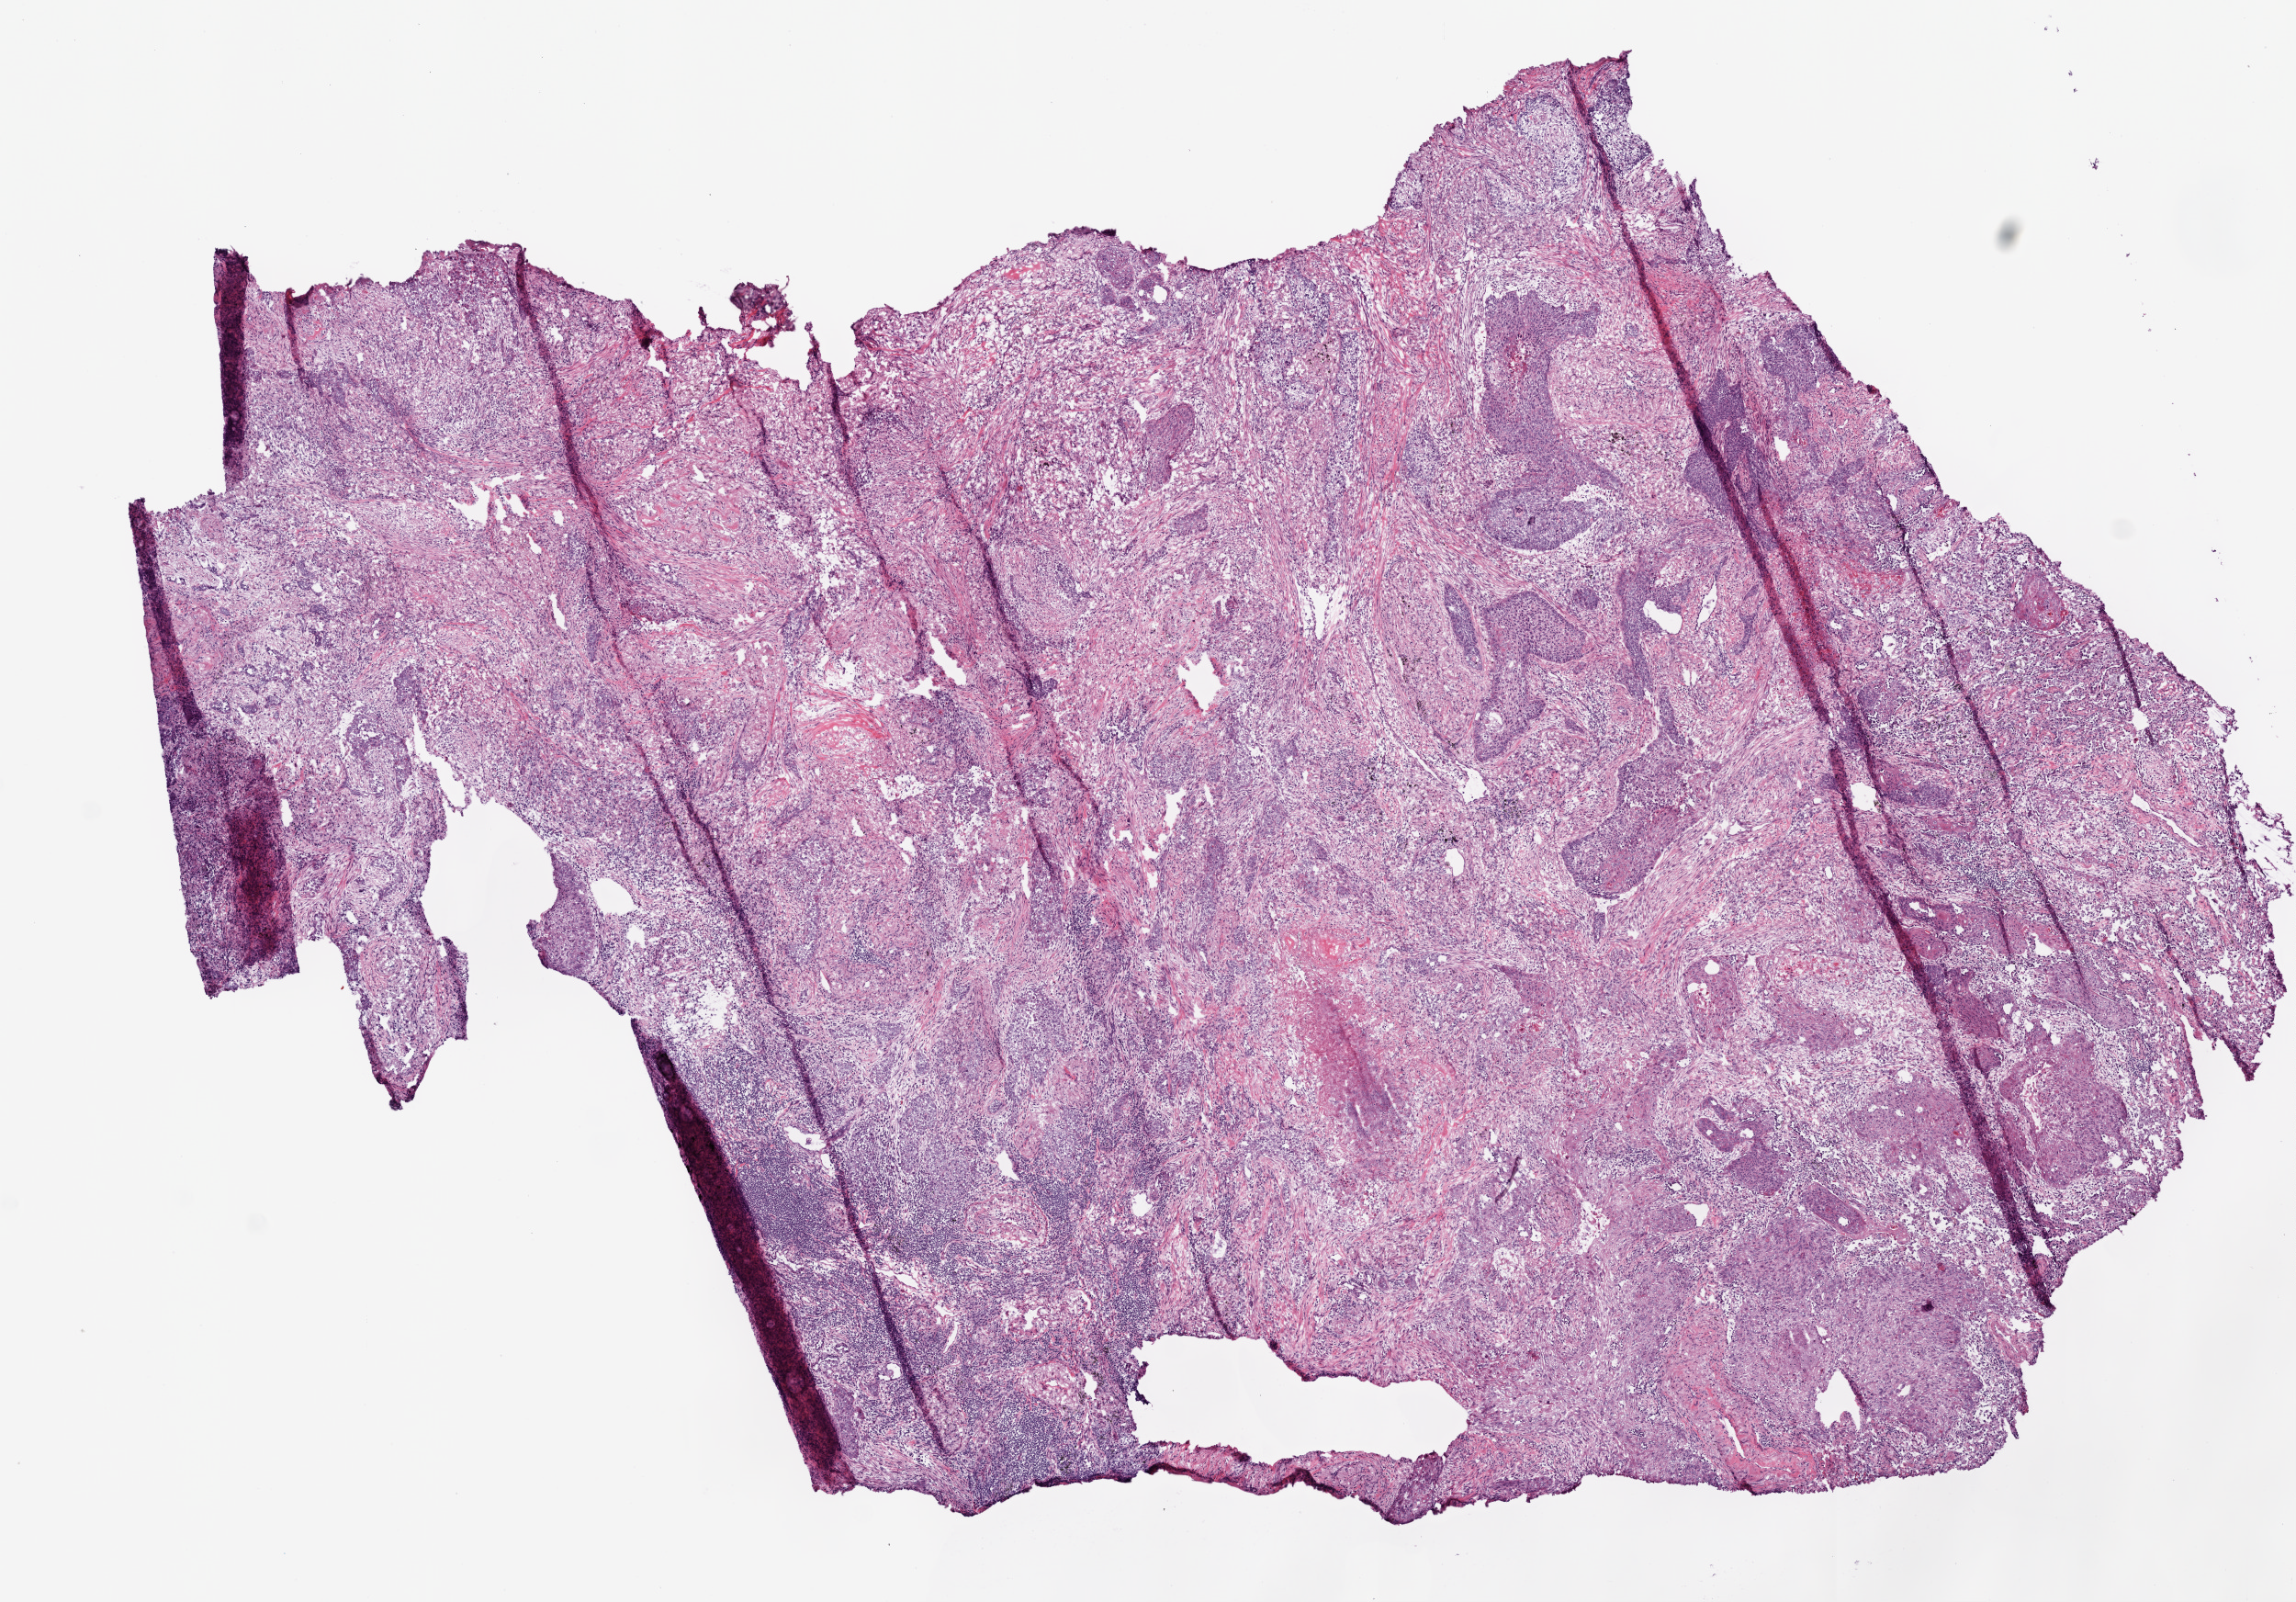
Whole-slide histology image, Hematoxylin and eosin (H&E) stained, a low-resolution overview of the entire scanned area, about 10.0 x 7.0 mm (from a 20x scan); frozen section from the top of the tissue portion; primary tumour sample from the lung. Patient: male, age at initial diagnosis 76 years. Composition of this section per pathologist review: tumour cells 65%, tumour nuclei 70%, normal cells 0%, stromal cells 30%, necrosis 5%.
• diagnosis: Squamous cell carcinoma, NOS (lower lobe, lung)
• laterality: left
• TNM: T1a N0 M0
• AJCC pathologic stage: IA